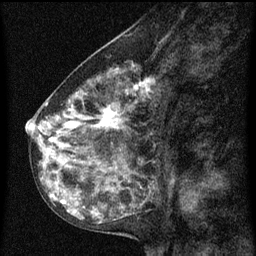
Breast MRI (dynamic contrast-enhanced), one sagittal slice. Position 34 of 60 along the scan axis. Dynamic contrast-enhanced series, image 2 of 3 at this slice position (ordered by acquisition). 1.5 T. TE 4.2 ms, TR 8 ms. 2 mm slice thickness. 256 × 256 image matrix, field of view 180 × 180 mm. Patient: female, 55 years.
Outlined on this slice (semi-automatically segmented with operator editing):
- analysis volume of interest (the breast-tissue region the enhancement analysis was run in; not a lesion): bounding box (x1, y1, x2, y2) in pixels: (34, 68, 159, 151)
- tumour enhancement mask (voxels above the 70 % enhancement threshold inside the analysis volume of interest): (38, 72, 153, 147)